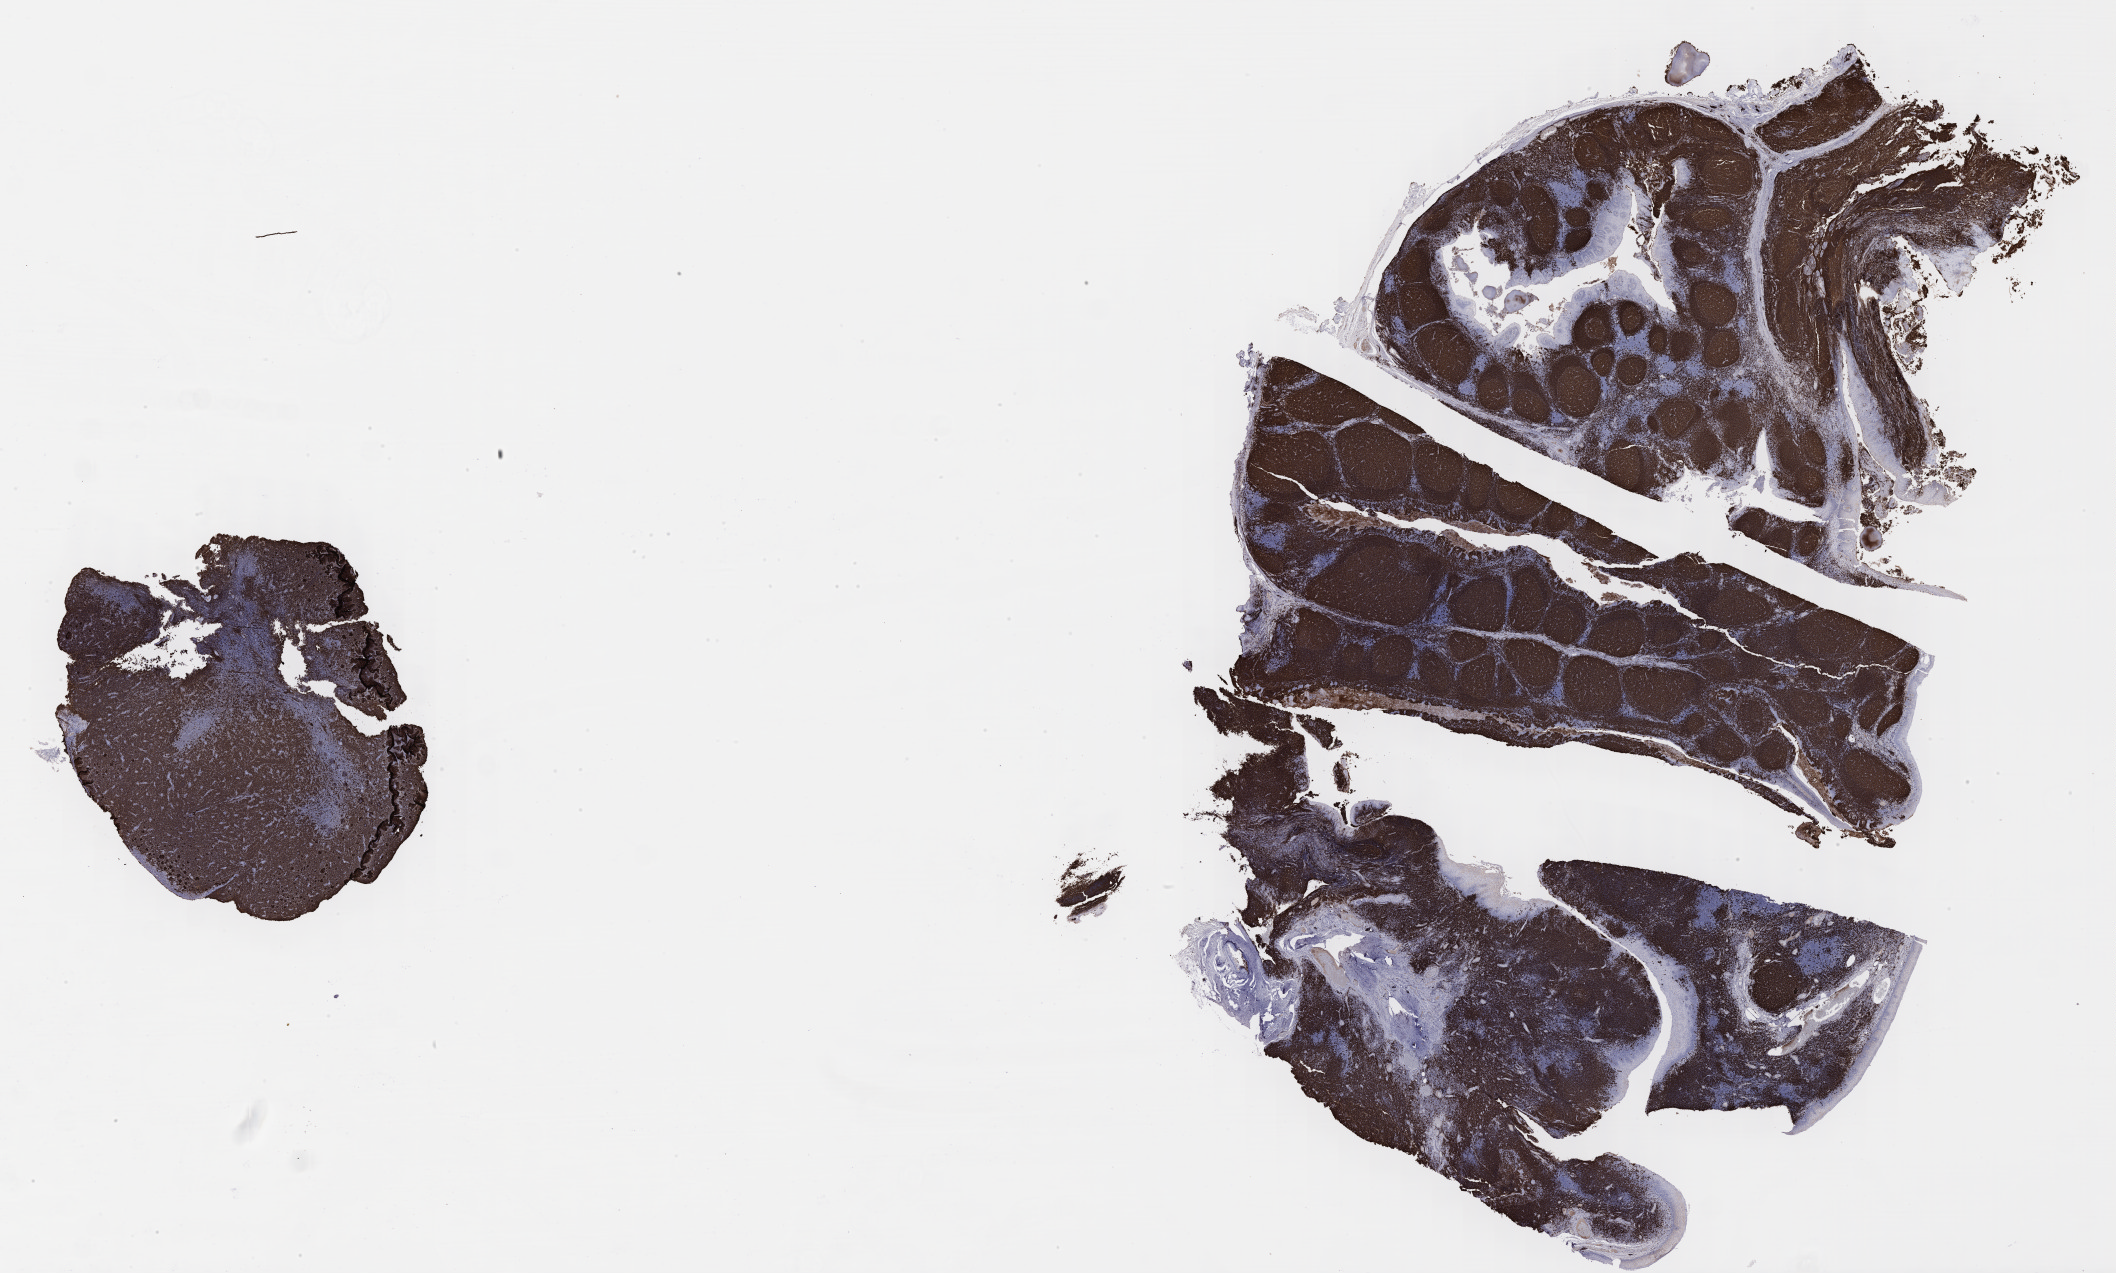
IHC for CD20, whole-slide image — low-resolution overview of the scanned area, about 34.2 x 20.6 mm, specimen: tumor tissue, anatomic site: liver. Patient male; age 46 years.
Diagnosis: Diffuse large B-cell lymphoma, NOS.